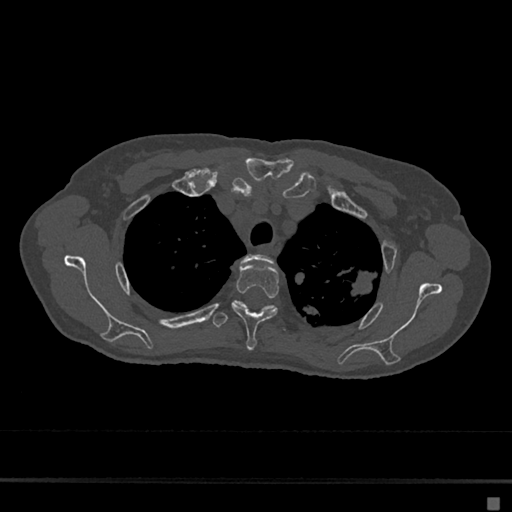
CT including the spine, one axial slice; slice 533 of 797 in the series (ordered by position); 120 kVp; bone window (W 1800 / L 400 HU); 512 × 512 image matrix. Patient: female, 68 years. From the clinical record (not read from this slice): primary cancer: renal.
Outlined on this slice (semi-automatic segmentation, software-assisted and operator-edited):
- T2 vertebra: box from (x=232, y=254) to (x=273, y=307) px
- T3 vertebra: (x=232, y=265)–(x=279, y=351)
- T4 vertebra: (x=212, y=305)–(x=287, y=332)